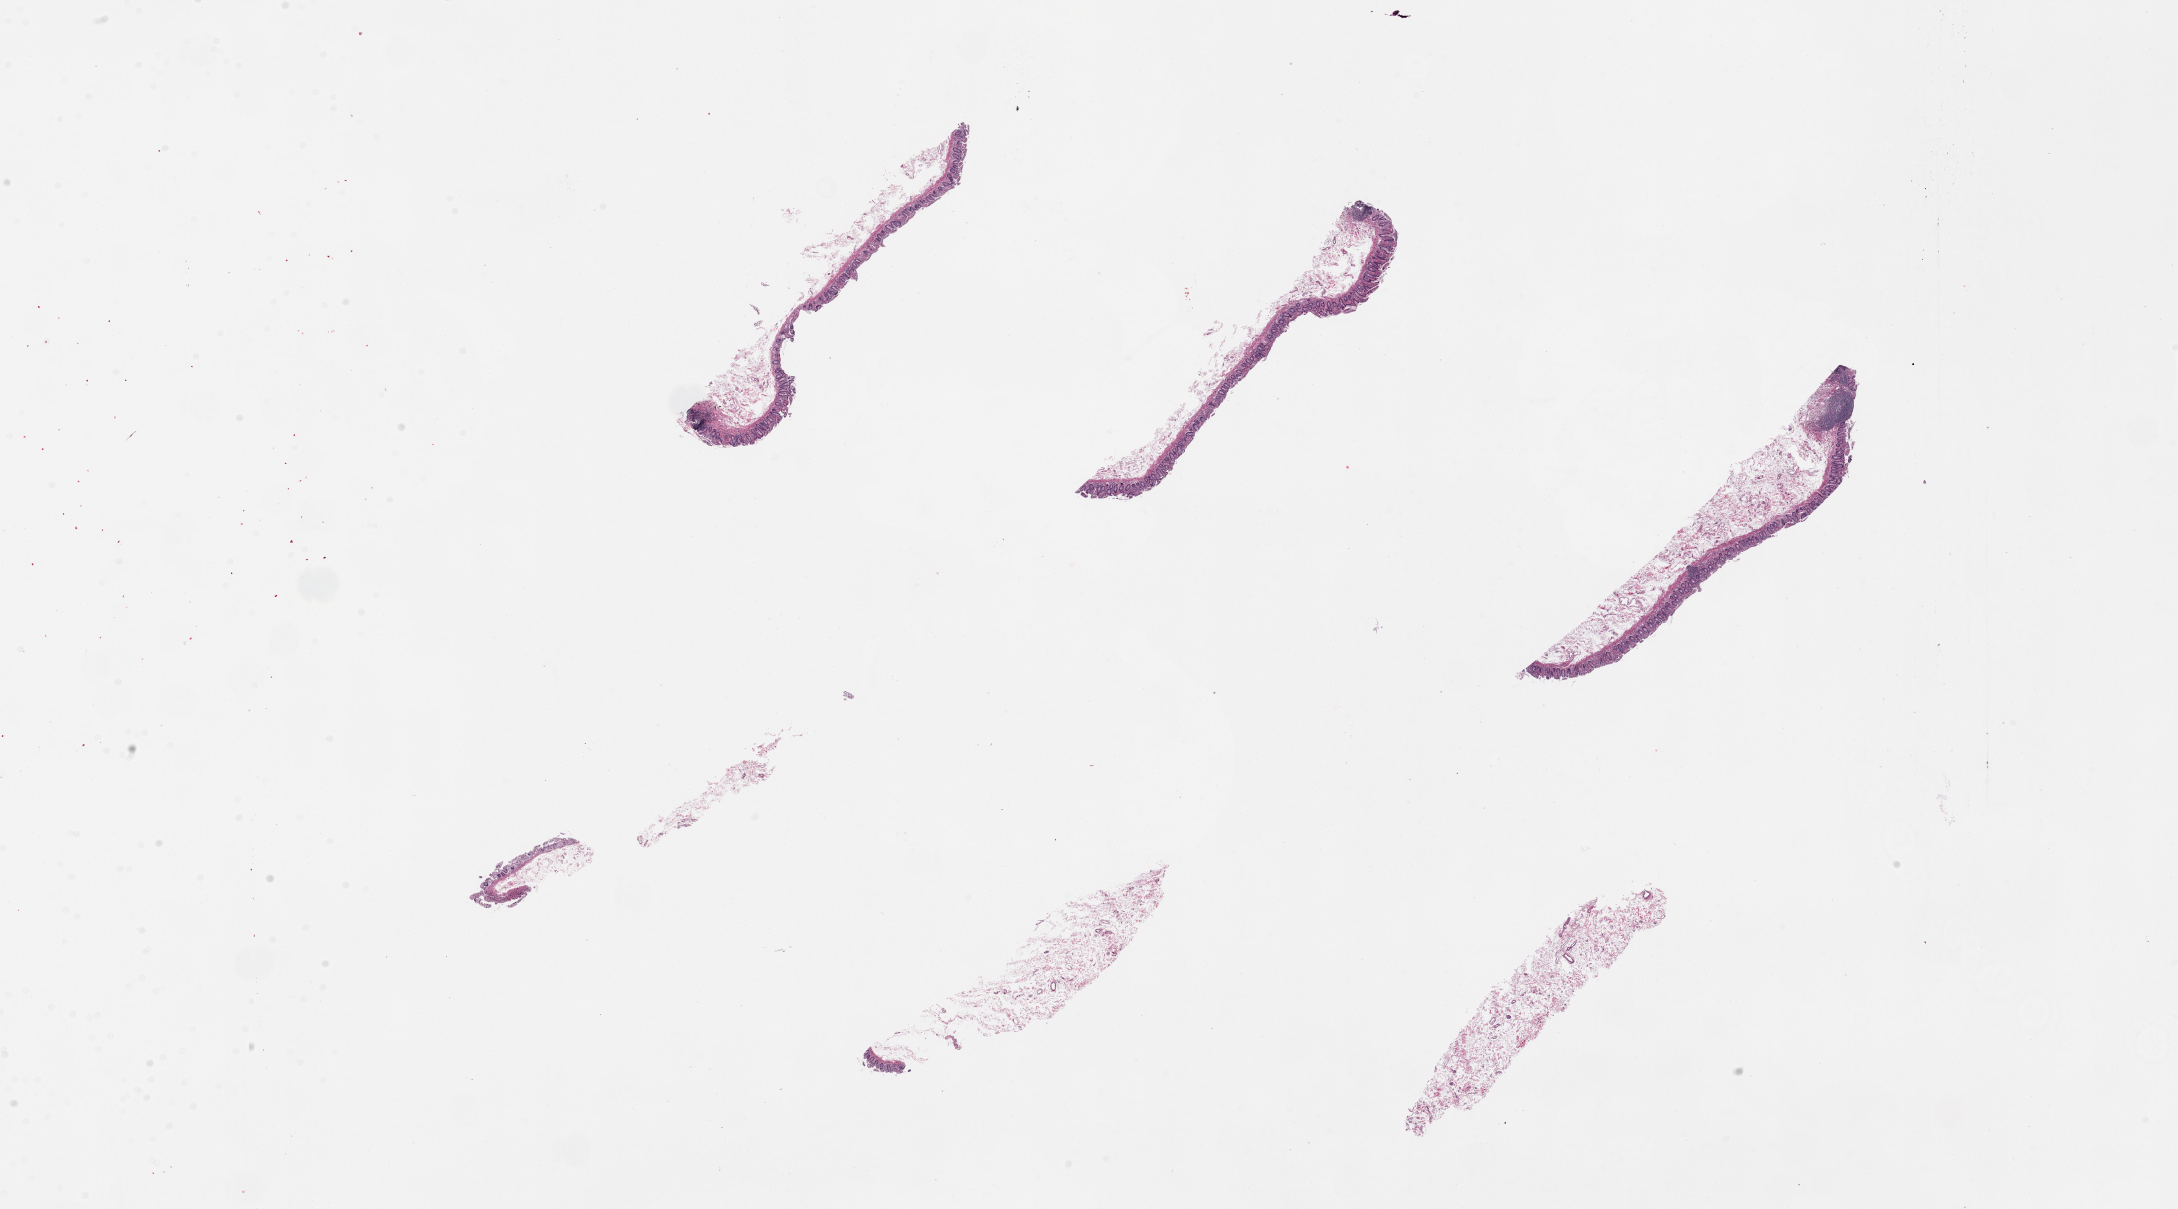
Whole-slide image, haematoxylin and eosin stain, brightfield, low-resolution overview of the scanned area, about 34.5 x 19.1 mm (slide scanned at 20x); PAXgene-fixed, paraffin-embedded tissue; target tissue: ileum; donor tissue sample. Female donor.
Pathologist's review note for this sample: 6 pieces. up to 7x2mm; 1 small lymphoid nodule in each of 3 pieces. Dissection good: no muscularis. 3 are mainly submucosa.